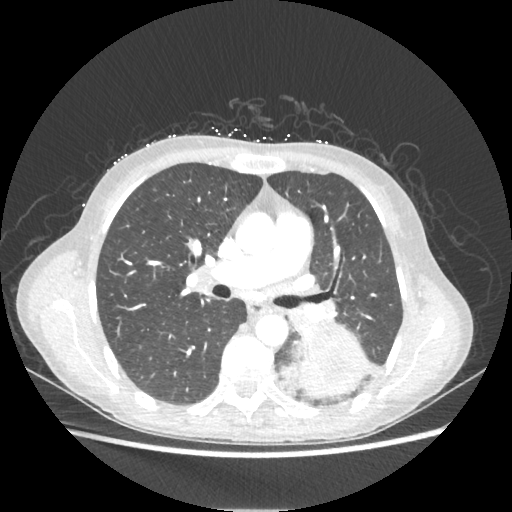
Chest CT, one axial slice; slice 128 of 221 in the series (ordered by position); lung window (W 1500 / L -600 HU); 1.25 mm slice thickness; 512 × 512 image matrix, field of view 360 × 360 mm. Patient: female, 53 years. Case-level facts recorded for this patient, not image findings: clinical TNM (as recorded): T3 N0 M0.
Structures marked on this image (rectangle marked by the reading radiologist):
- lung tumour (recorded histology: adenocarcinoma): box from (x=280, y=328) to (x=369, y=396) px